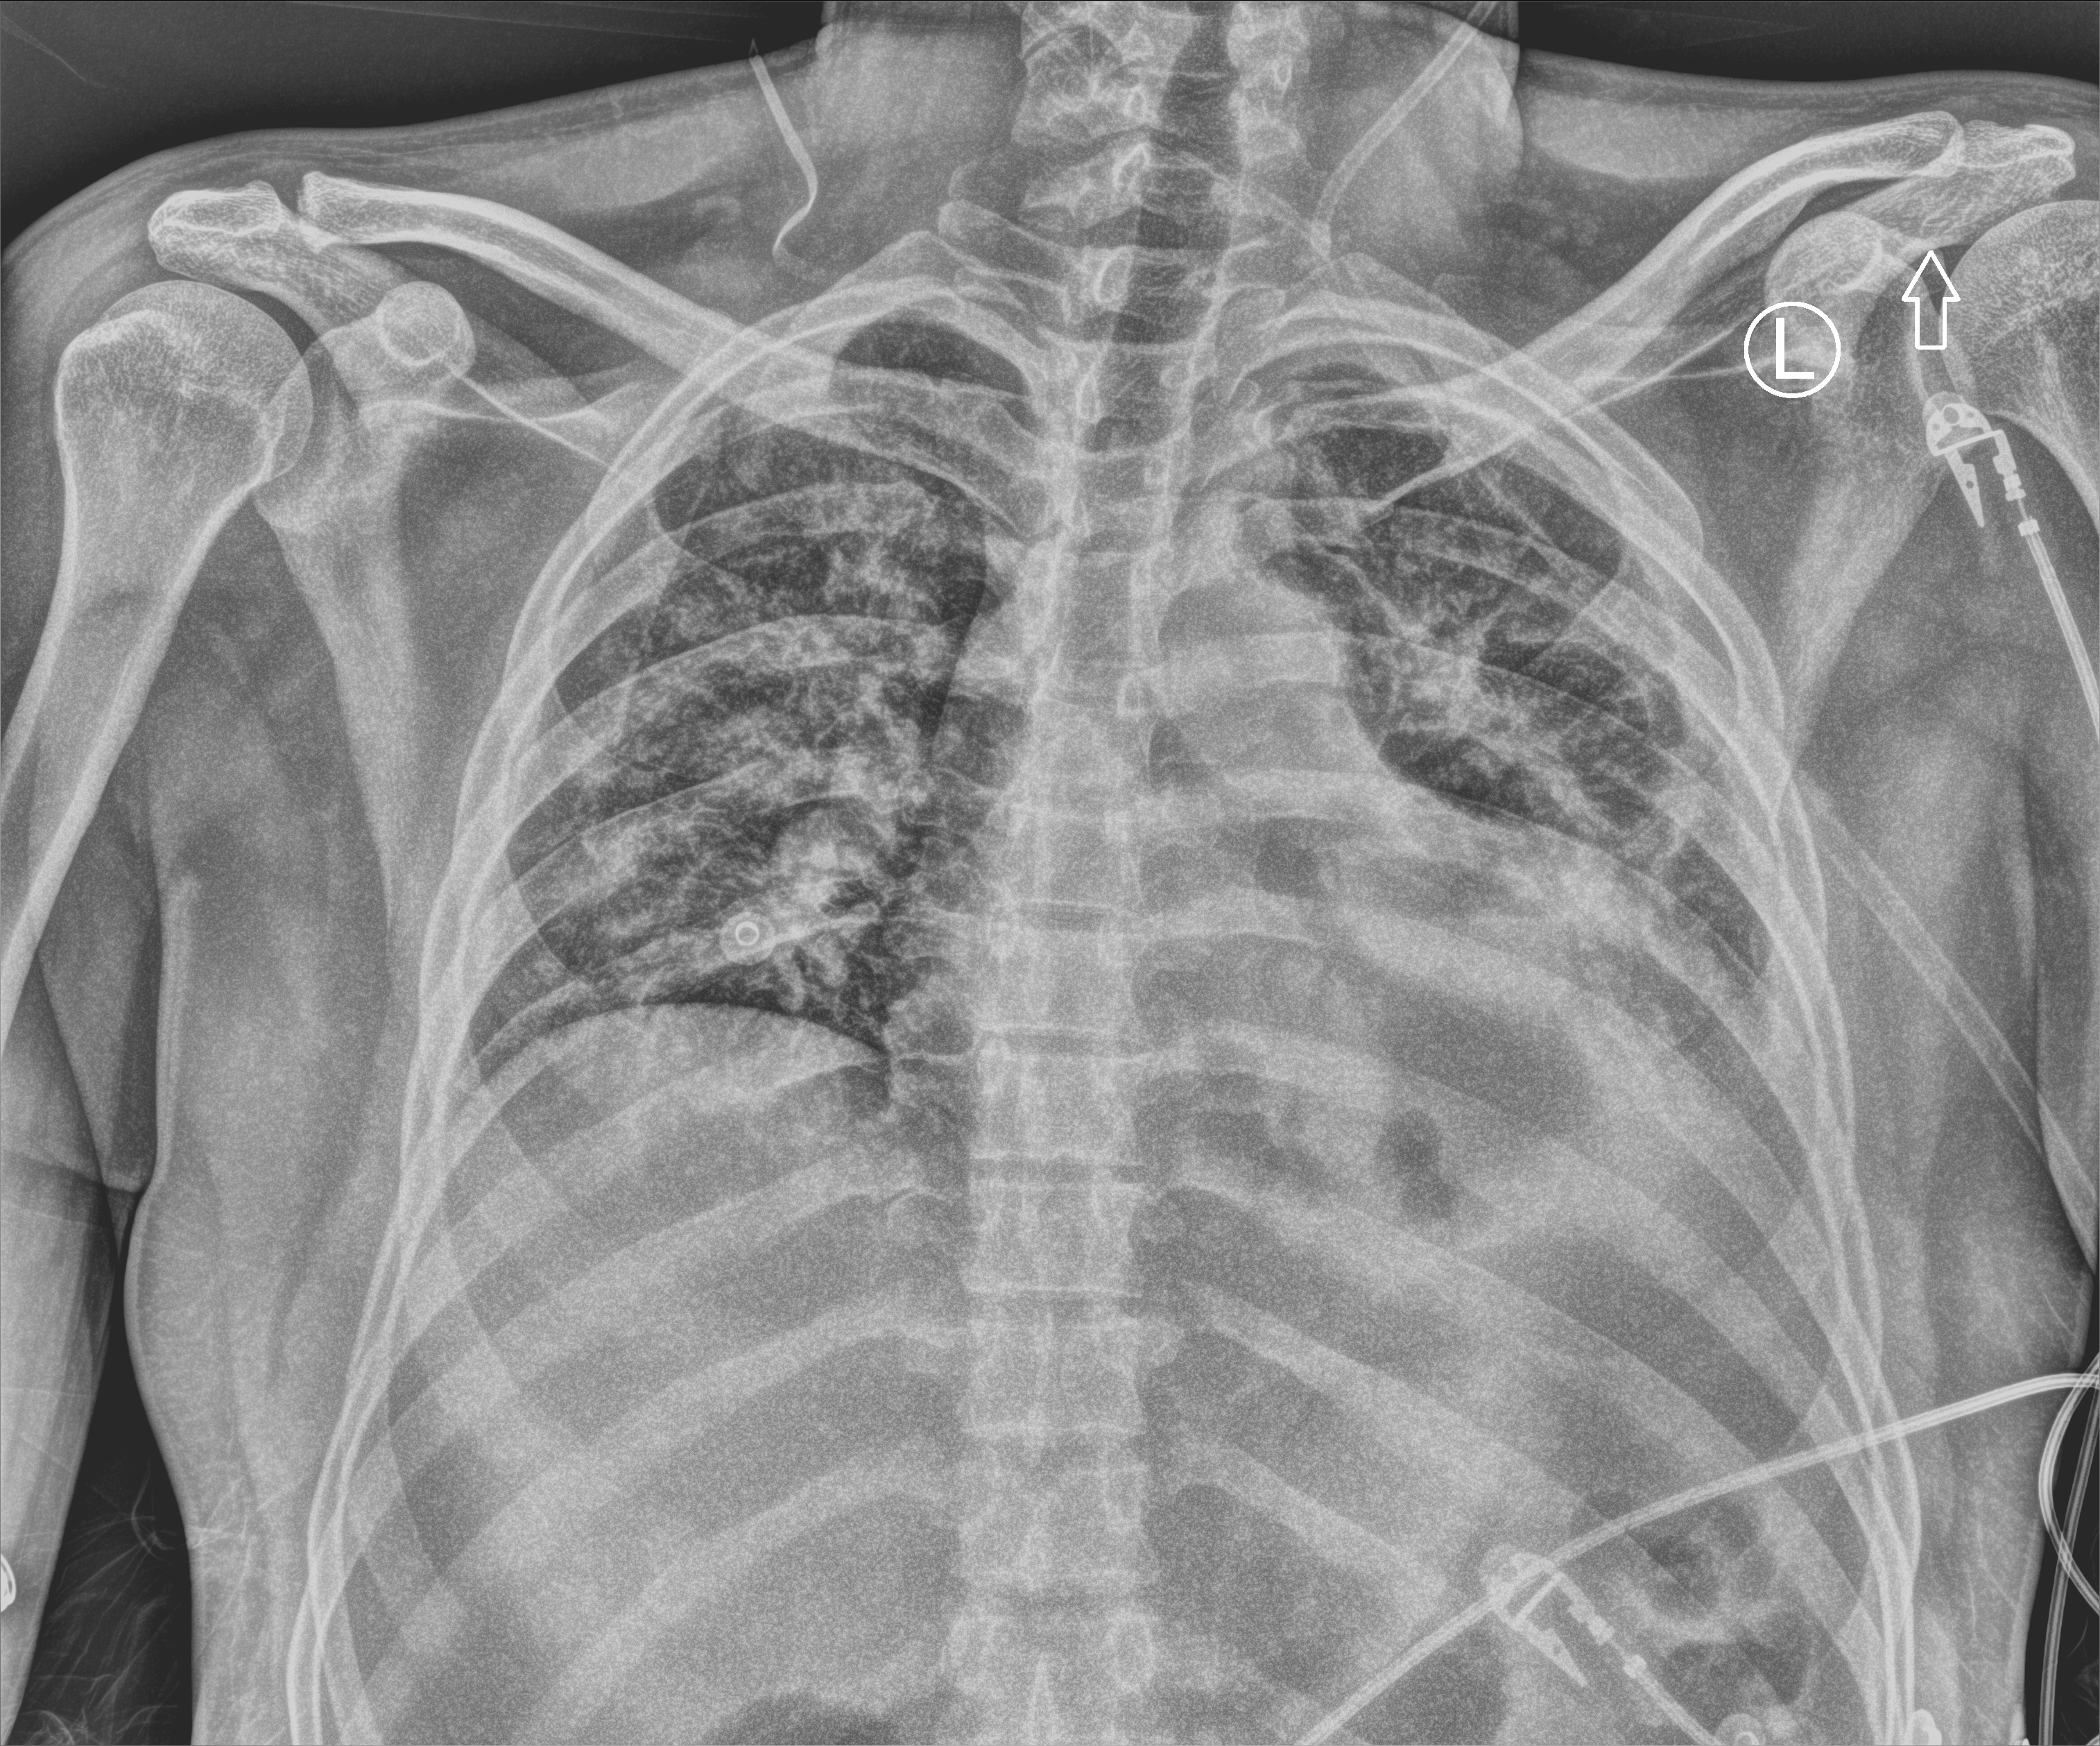
Chest X-ray (portable), anteroposterior (AP) projection. Male patient hospitalised with COVID-19, age 18–59 years.
Hospital-stay facts (about this admission, not read from this image; timing relative to this image not recorded):
- other chronic lung disease (admission record): no
- mechanically ventilated during this hospital stay: yes
- admitted to intensive care during this hospital stay: yes